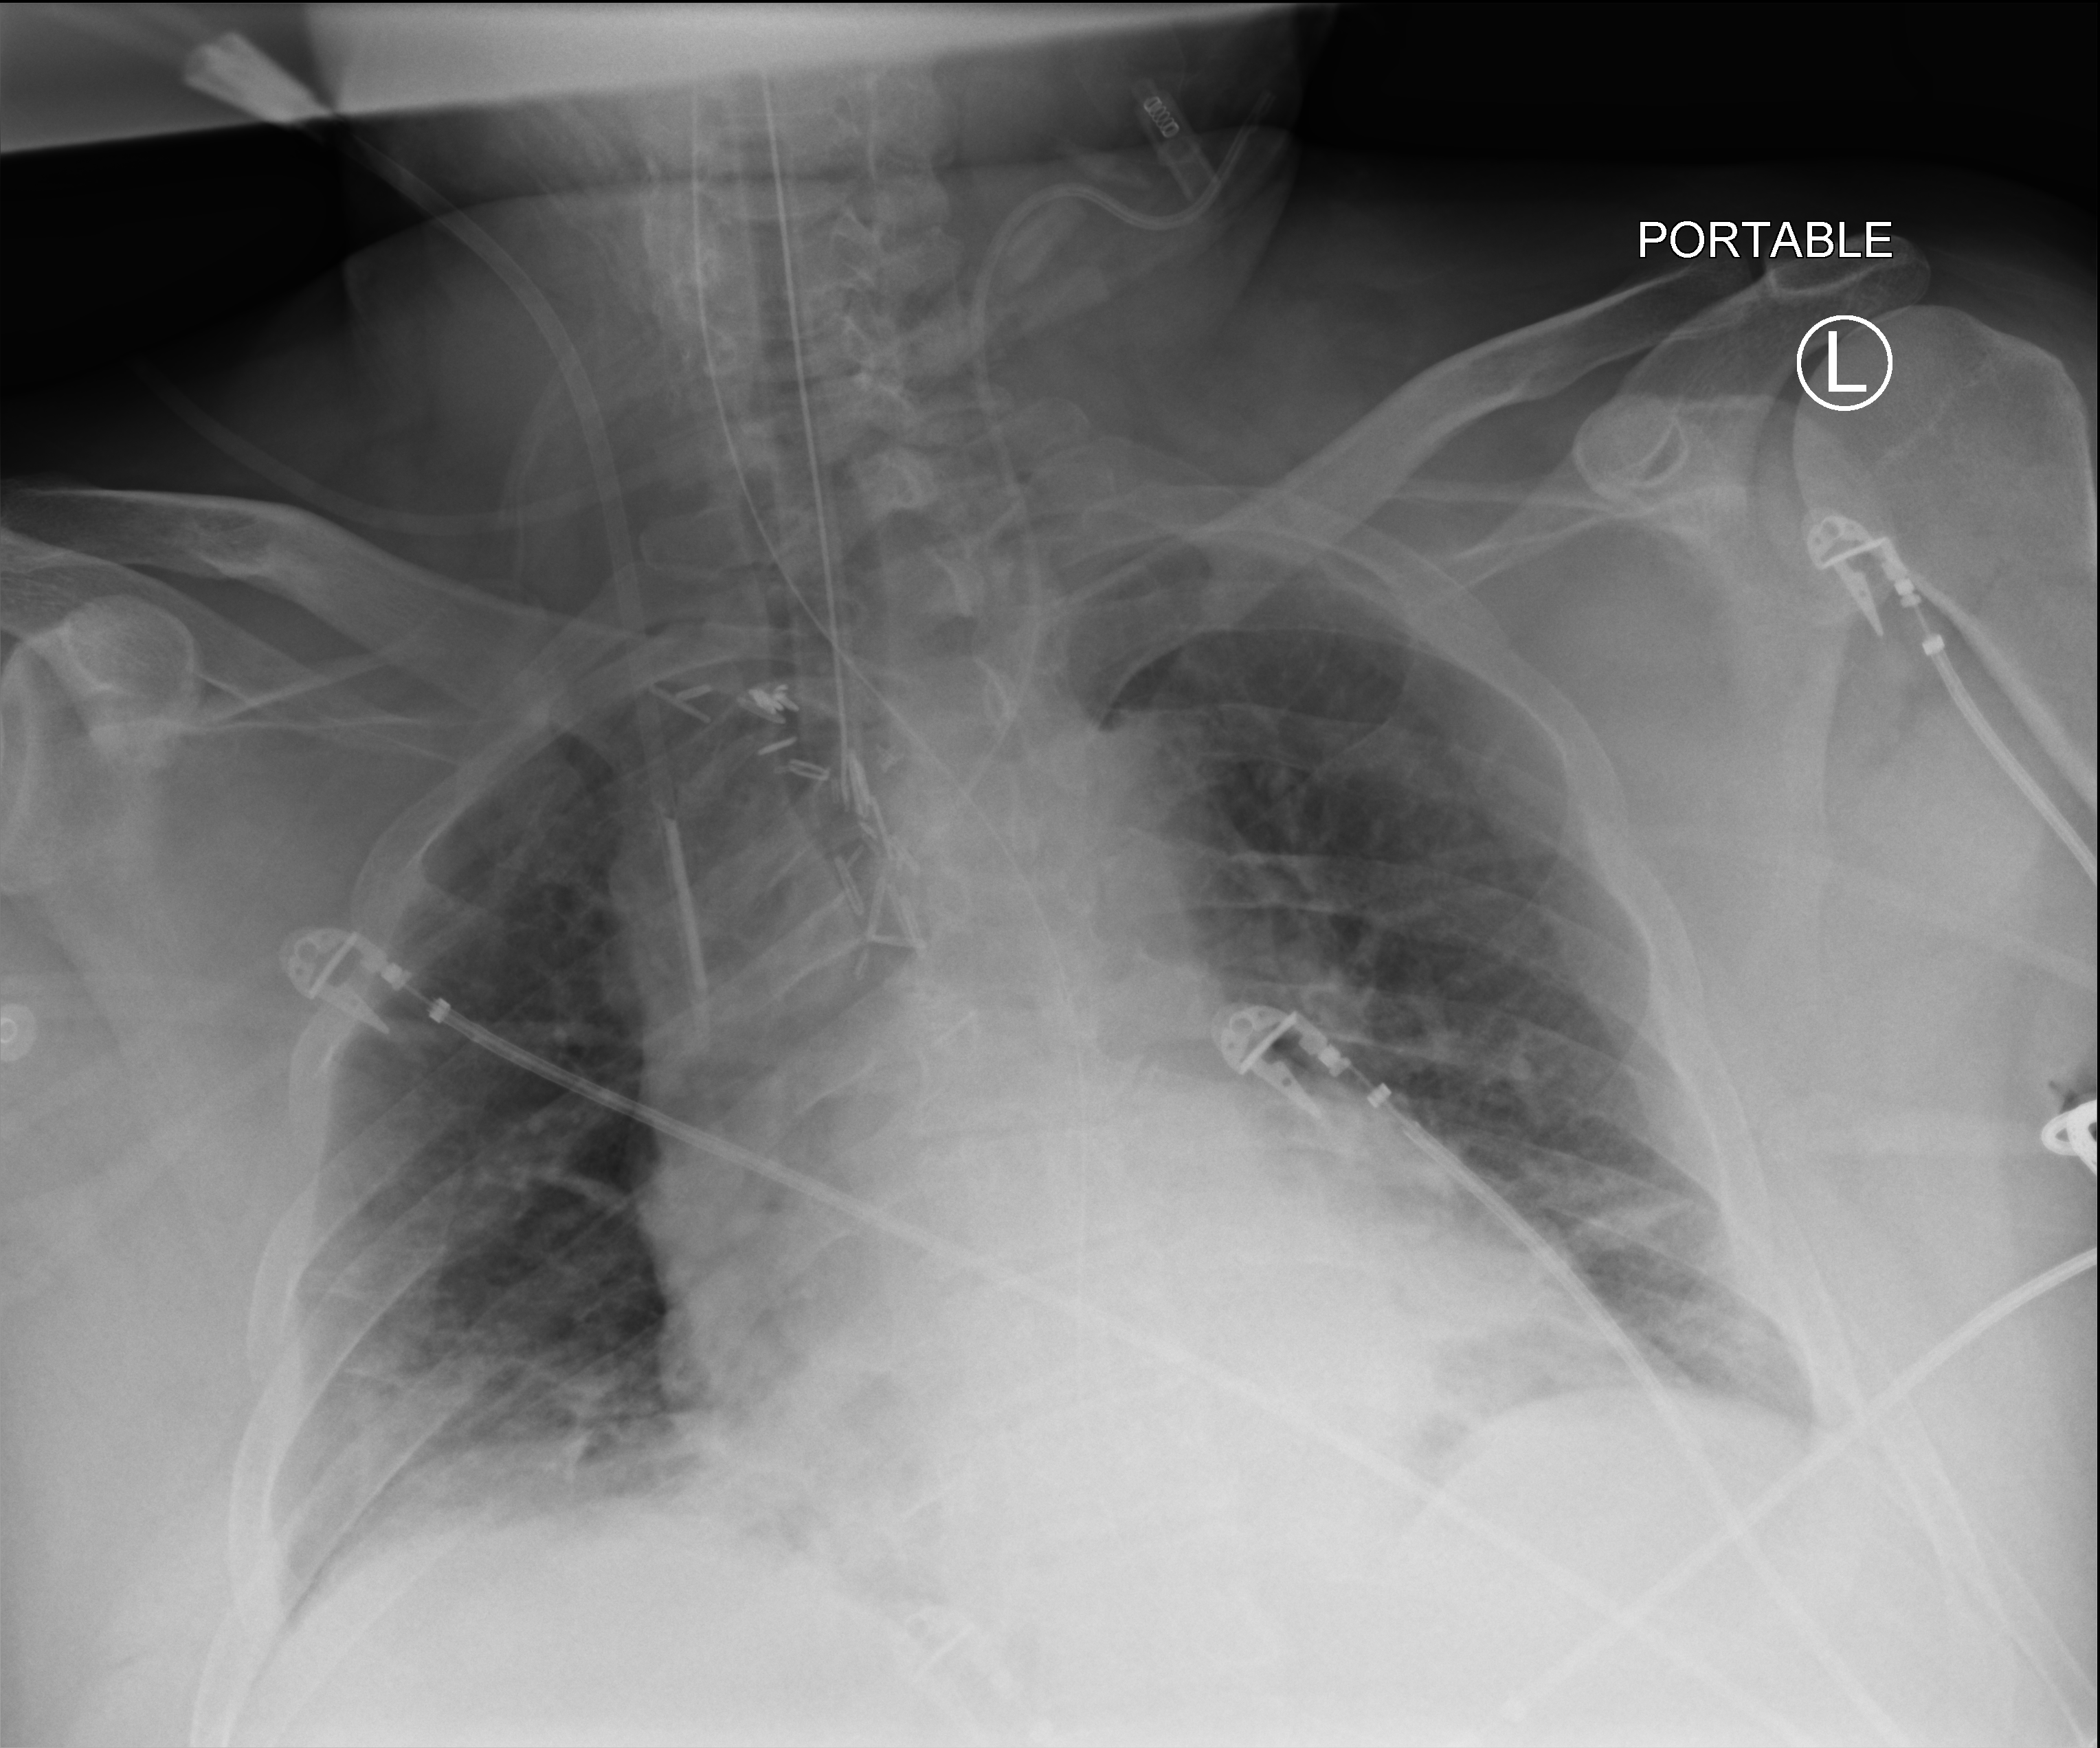
Bedside chest radiograph (computed radiography), anteroposterior (AP) projection. Patient hospitalised with COVID-19, aged 18–59 years.
From the hospital-stay record, not from the radiograph (when in the stay this image was taken is not recorded):
- admitted to intensive care during this hospital stay: yes